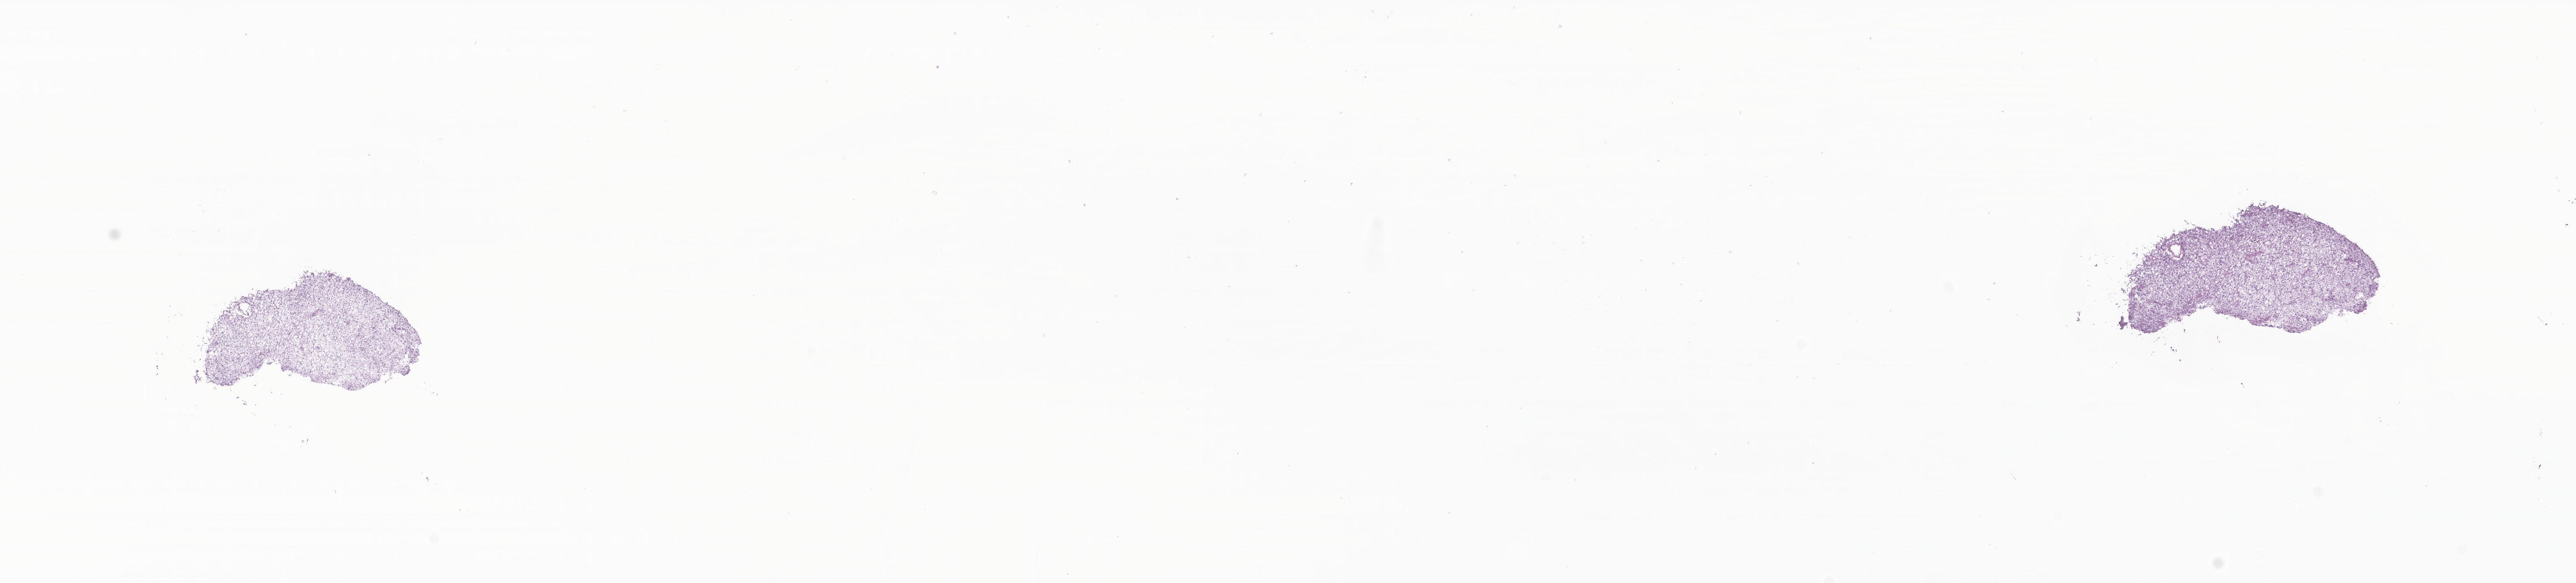
Whole-slide image, haematoxylin and eosin stain of tumor tissue from the brain — whole scanned area (about 24.5 x 5.5 mm) shown as a low-resolution overview. Cryosection (OCT / tissue freezing medium). Female patient, age 111 months (9 years 3 months).
Diagnosis: Pilocytic astrocytoma.